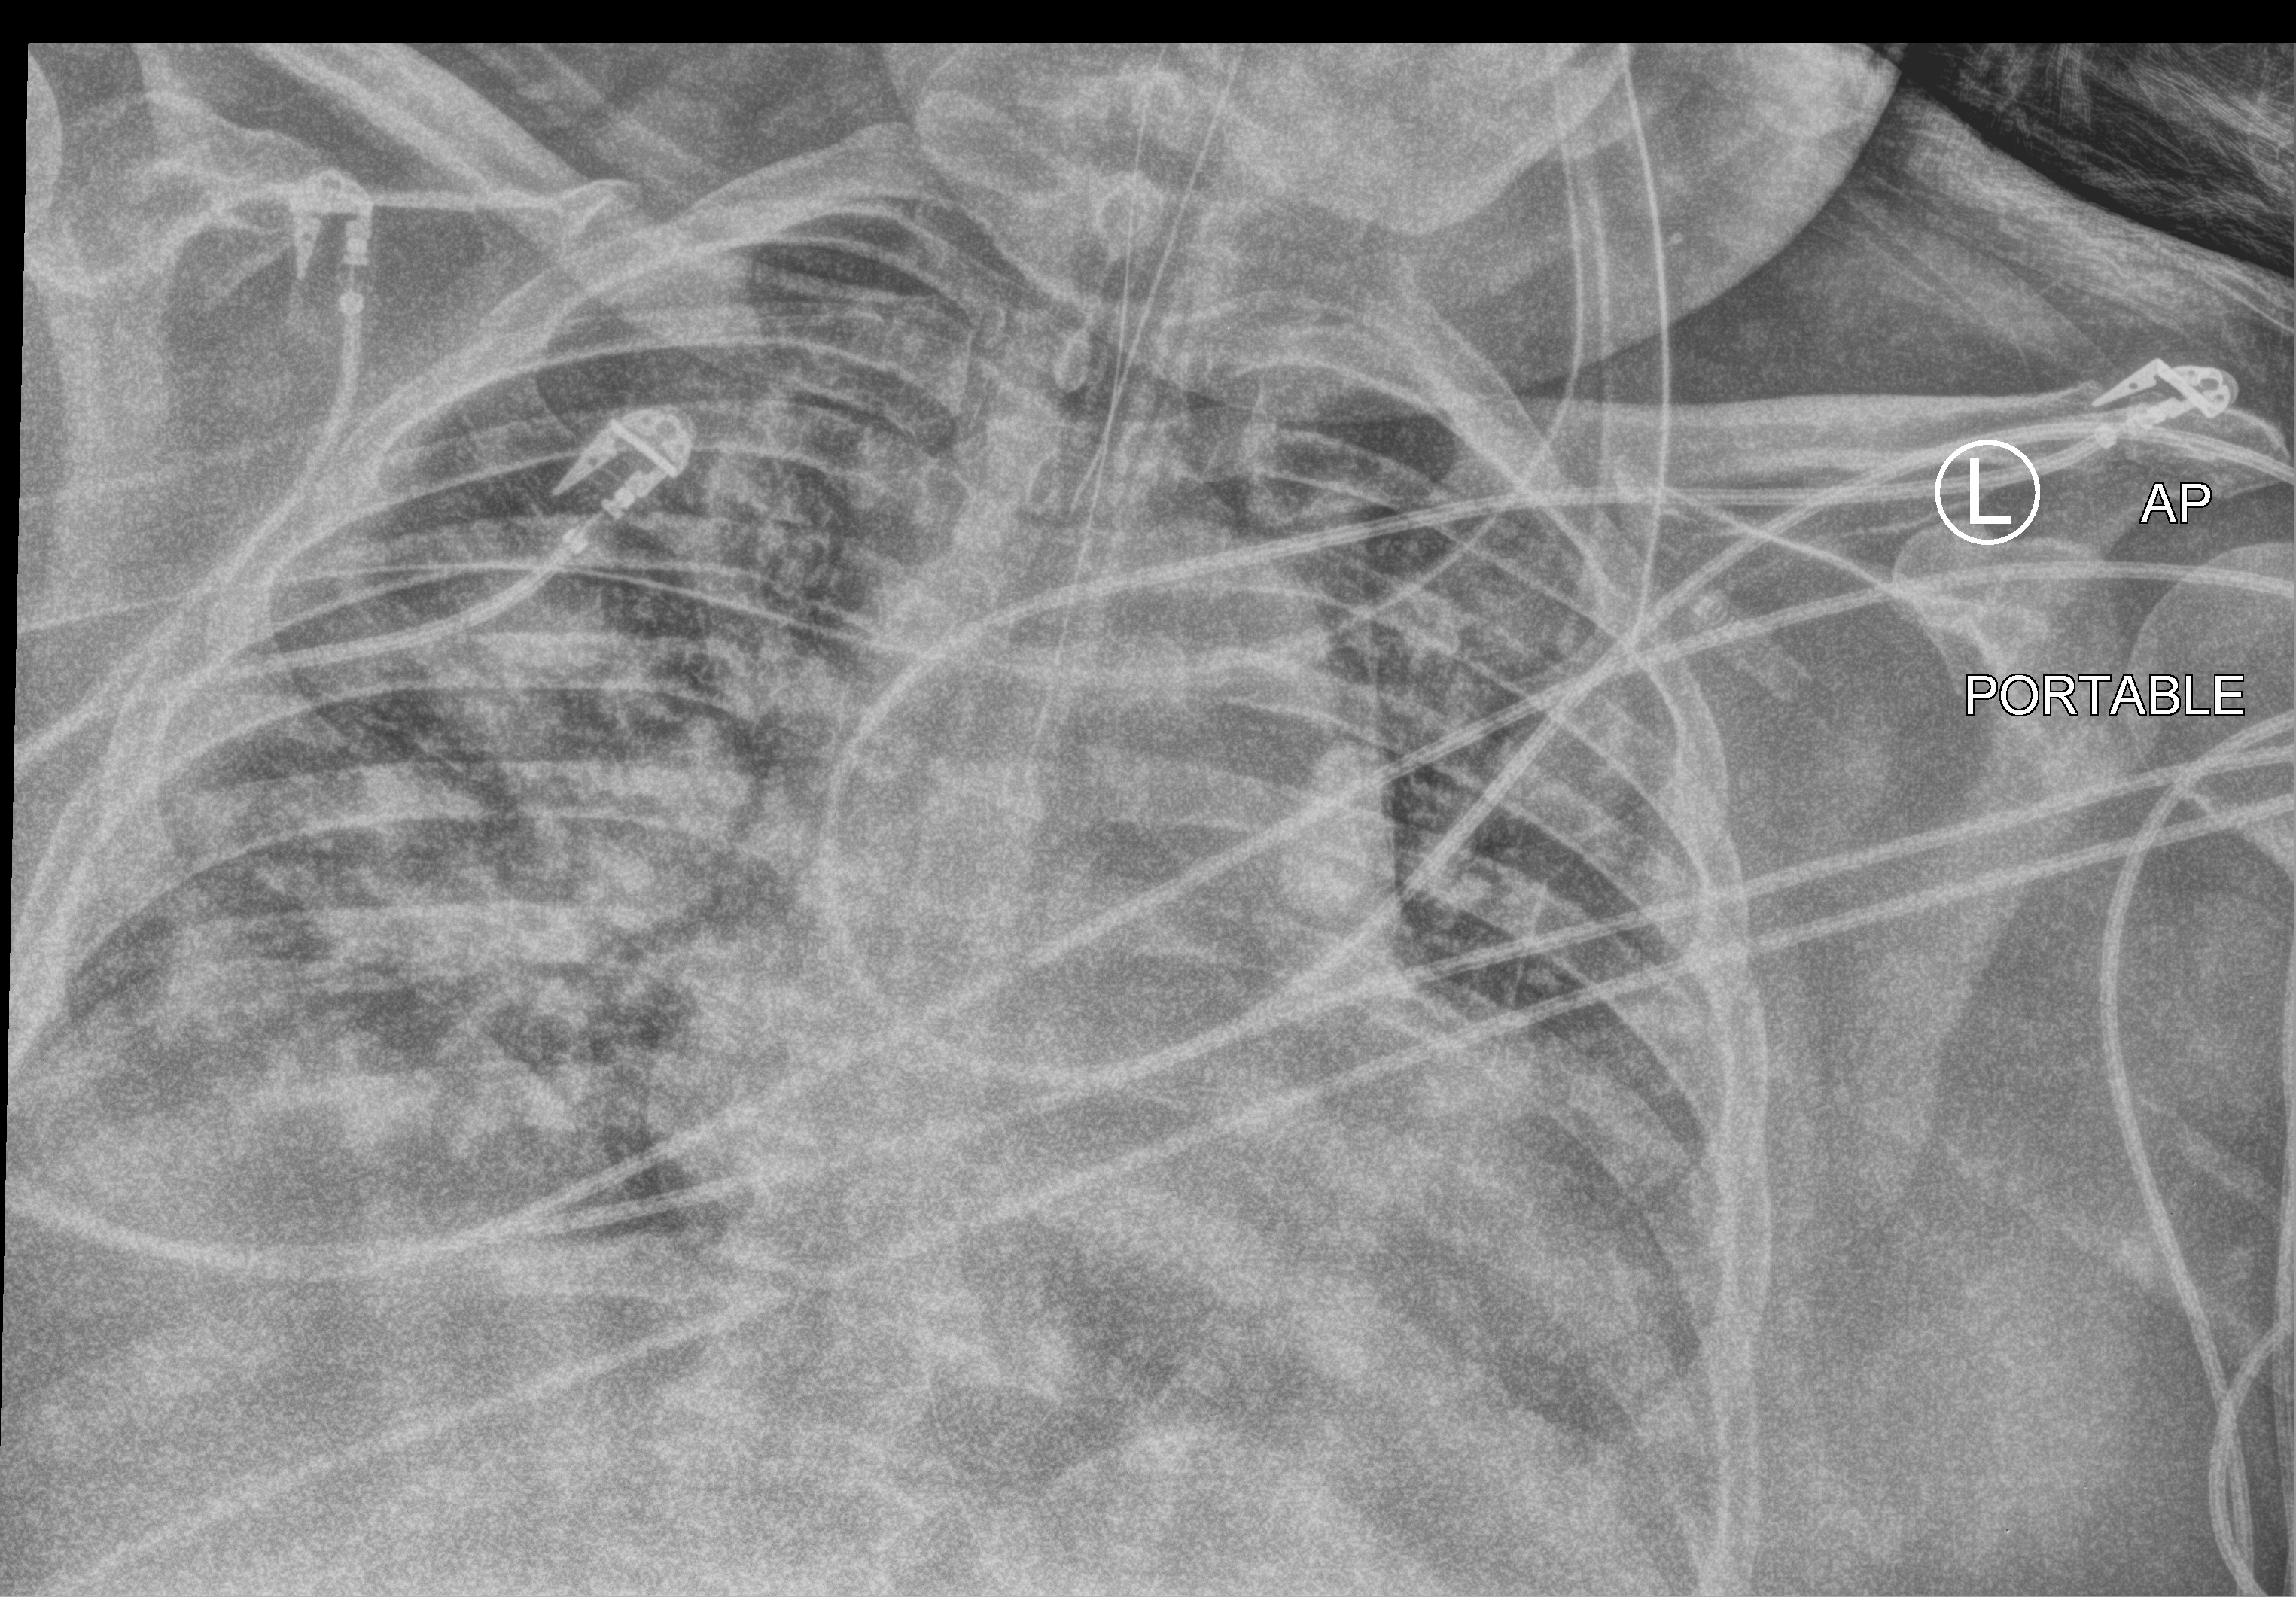
Portable chest radiograph, anteroposterior (AP) projection. Patient hospitalised with COVID-19; male, aged 18–59 years.
From the hospital-stay record, not from the radiograph (when in the stay this image was taken is not recorded):
- admitted to intensive care during this hospital stay: yes
- diabetes (admission record): yes